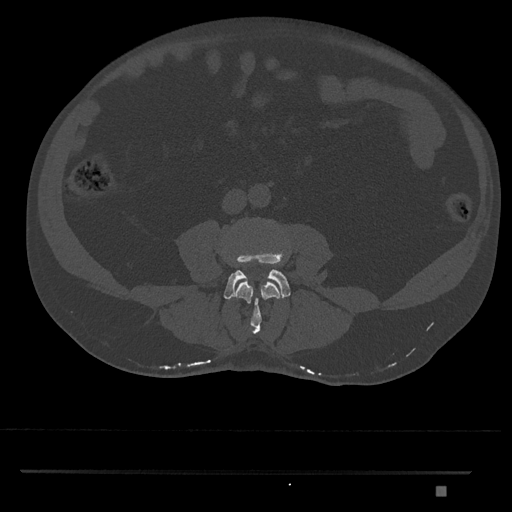
CT including the spine, one axial slice. Position 647 of 1134 along the scan axis. Reconstruction kernel Br40s/3. 120 kVp. Bone window (W 1800 / L 400 HU). 0.5 mm slice thickness. 512 × 512 image matrix, field of view 429 × 429 mm. Patient: male, 65 years. From the clinical record (not read from this slice): primary cancer: prostate.
Outlined on this slice (semi-automatic segmentation, software-assisted and operator-edited):
- L3 vertebra: bounding box [x1, y1, x2, y2] px = [234, 281, 280, 334]
- L4 vertebra: [224, 244, 291, 300]